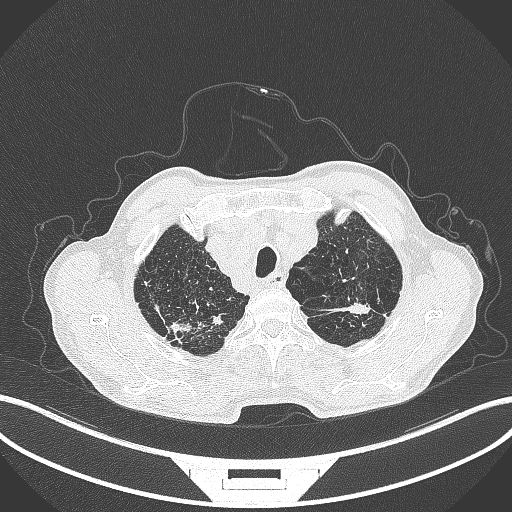
Chest CT, one axial slice. Position 385 of 463 along the scan axis. 120 kVp. Lung window (W 1500 / L -600 HU). 1 mm slice thickness. 512 × 512 image matrix, field of view 400 × 400 mm. Patient: male, 74 years. From the clinical record (not read from this slice): clinical TNM (as recorded): T2a N1 M0.
Structures marked on this image (bounding box drawn by a radiologist):
- lung tumour (recorded histology: adenocarcinoma): box from (x=330, y=297) to (x=377, y=318) px